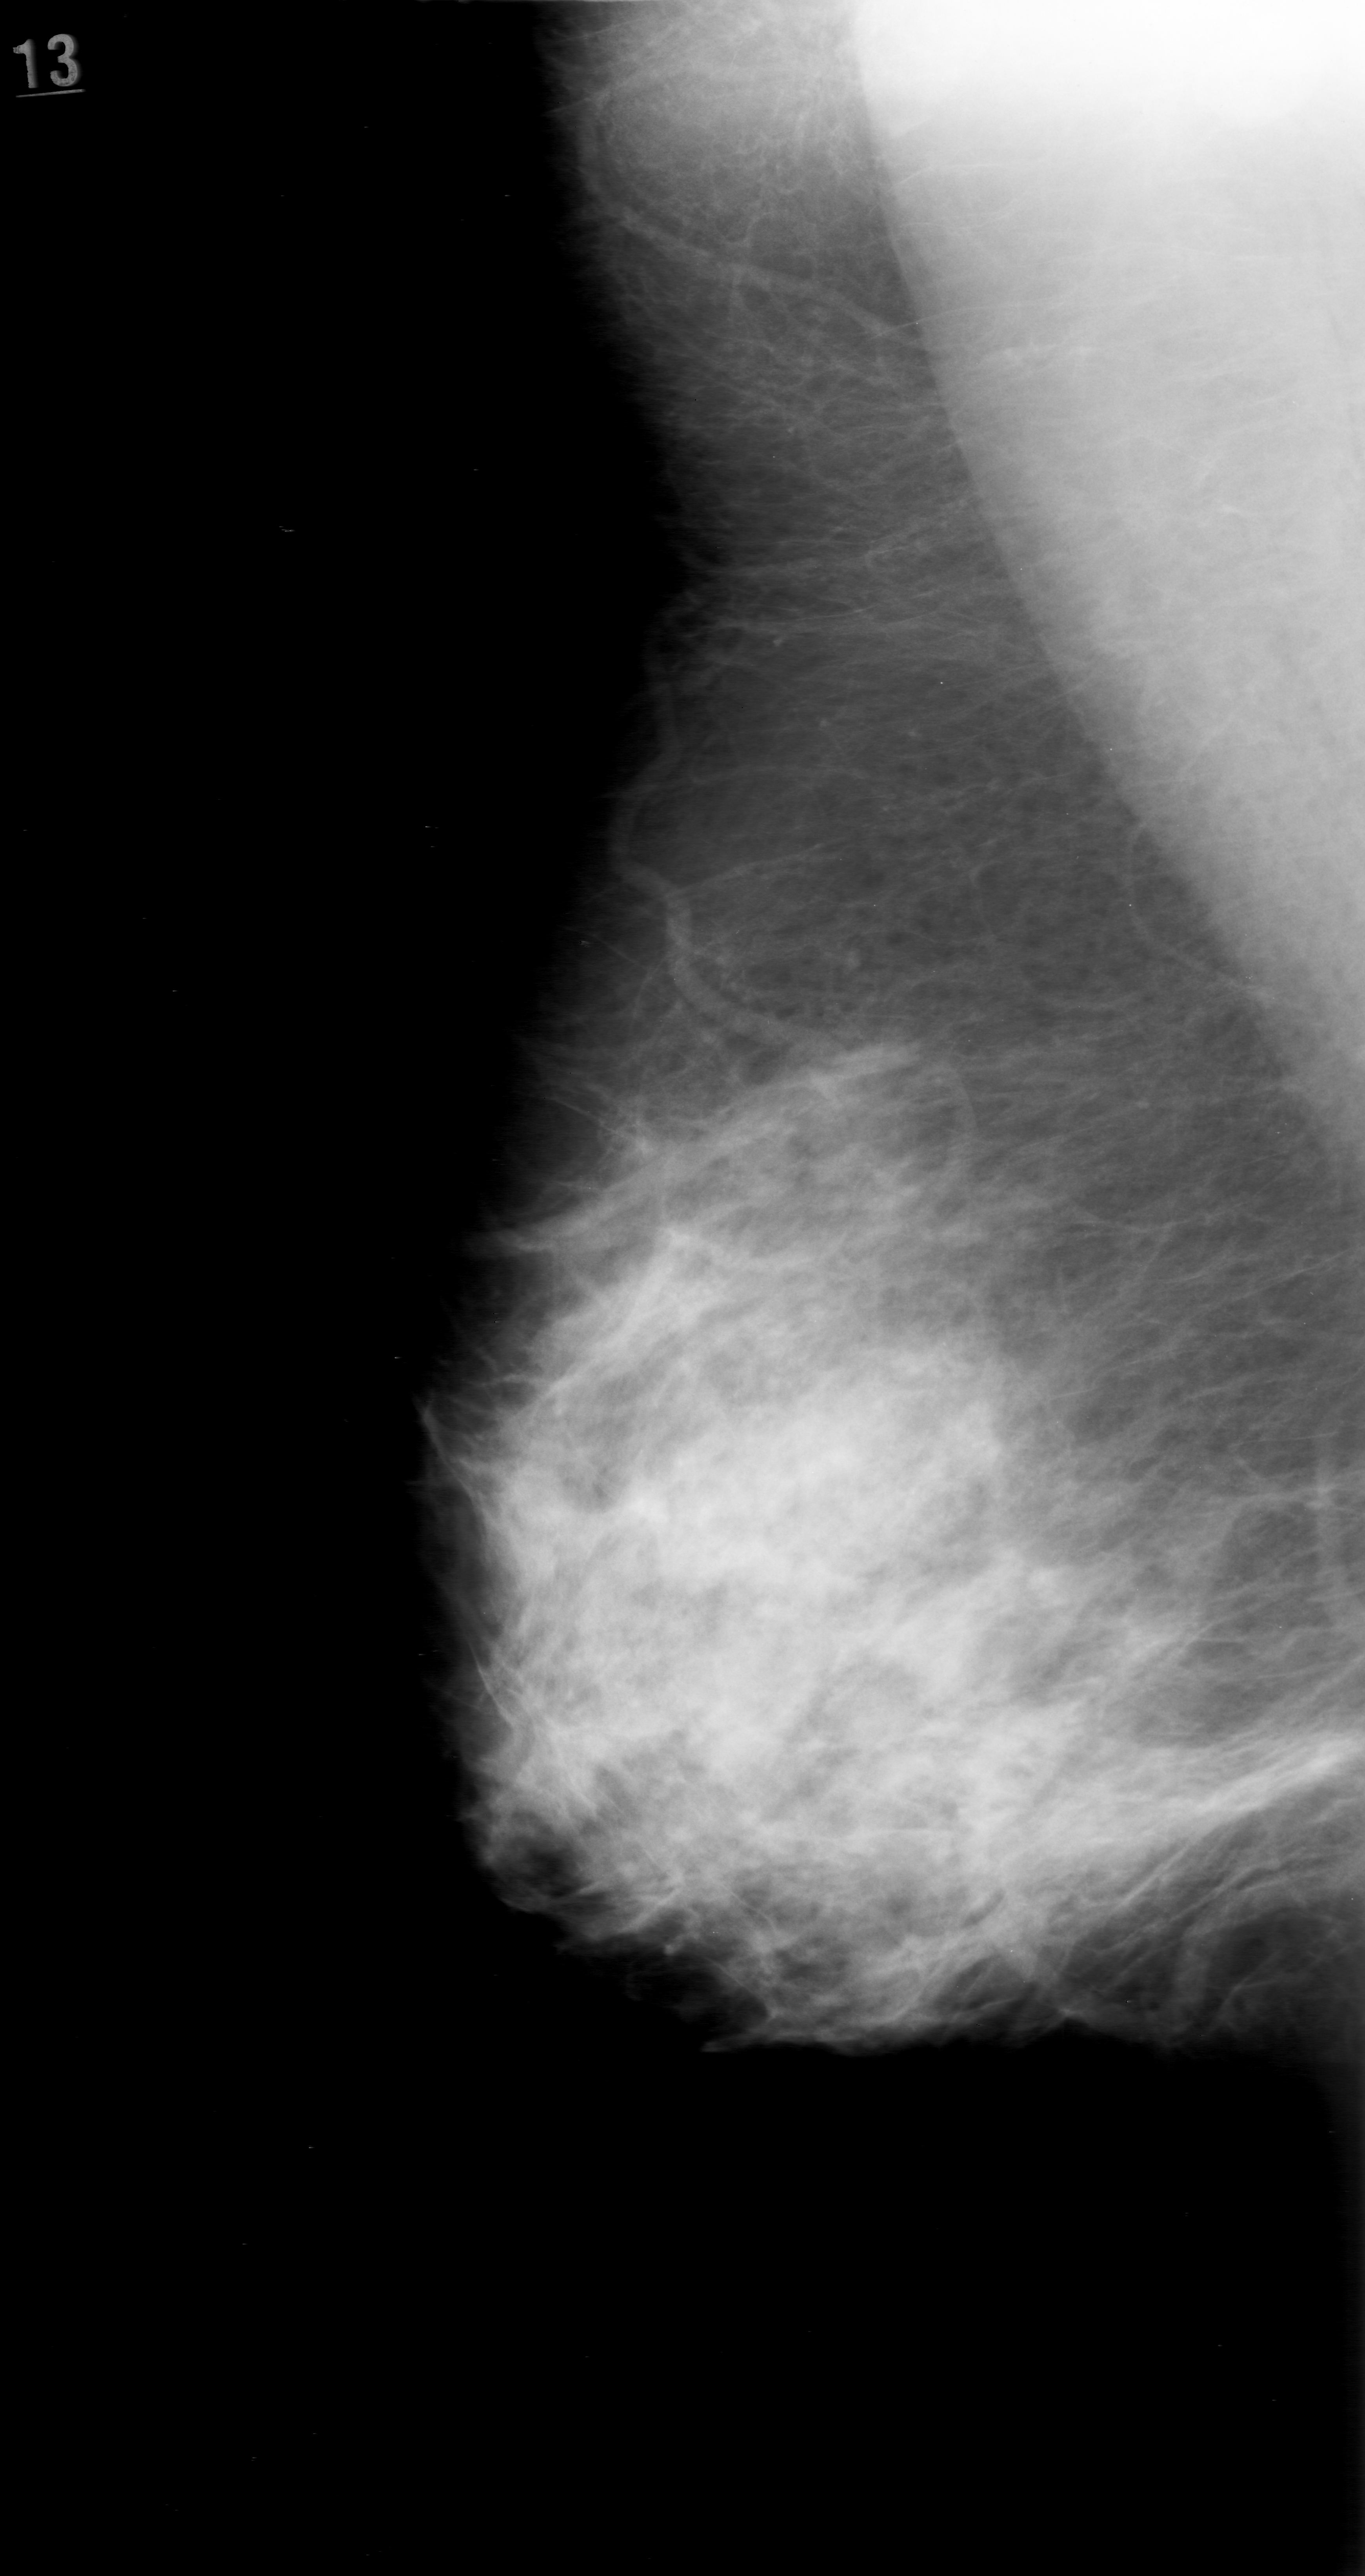
Scanned film-screen mammogram; right breast; mediolateral oblique (MLO) view; breast composition: heterogeneously dense (BI-RADS density category 3 of 4); 1365 × 2576 image matrix.
Expert-marked regions of interest on this image (one box per marked abnormality):
- calcifications, morphology punctate, distribution clustered; BI-RADS assessment category 0; subtlety rating 1 on a 1 (subtle) to 5 (obvious) scale; pathology (as recorded): benign: box from (x=577, y=1421) to (x=759, y=1609) px